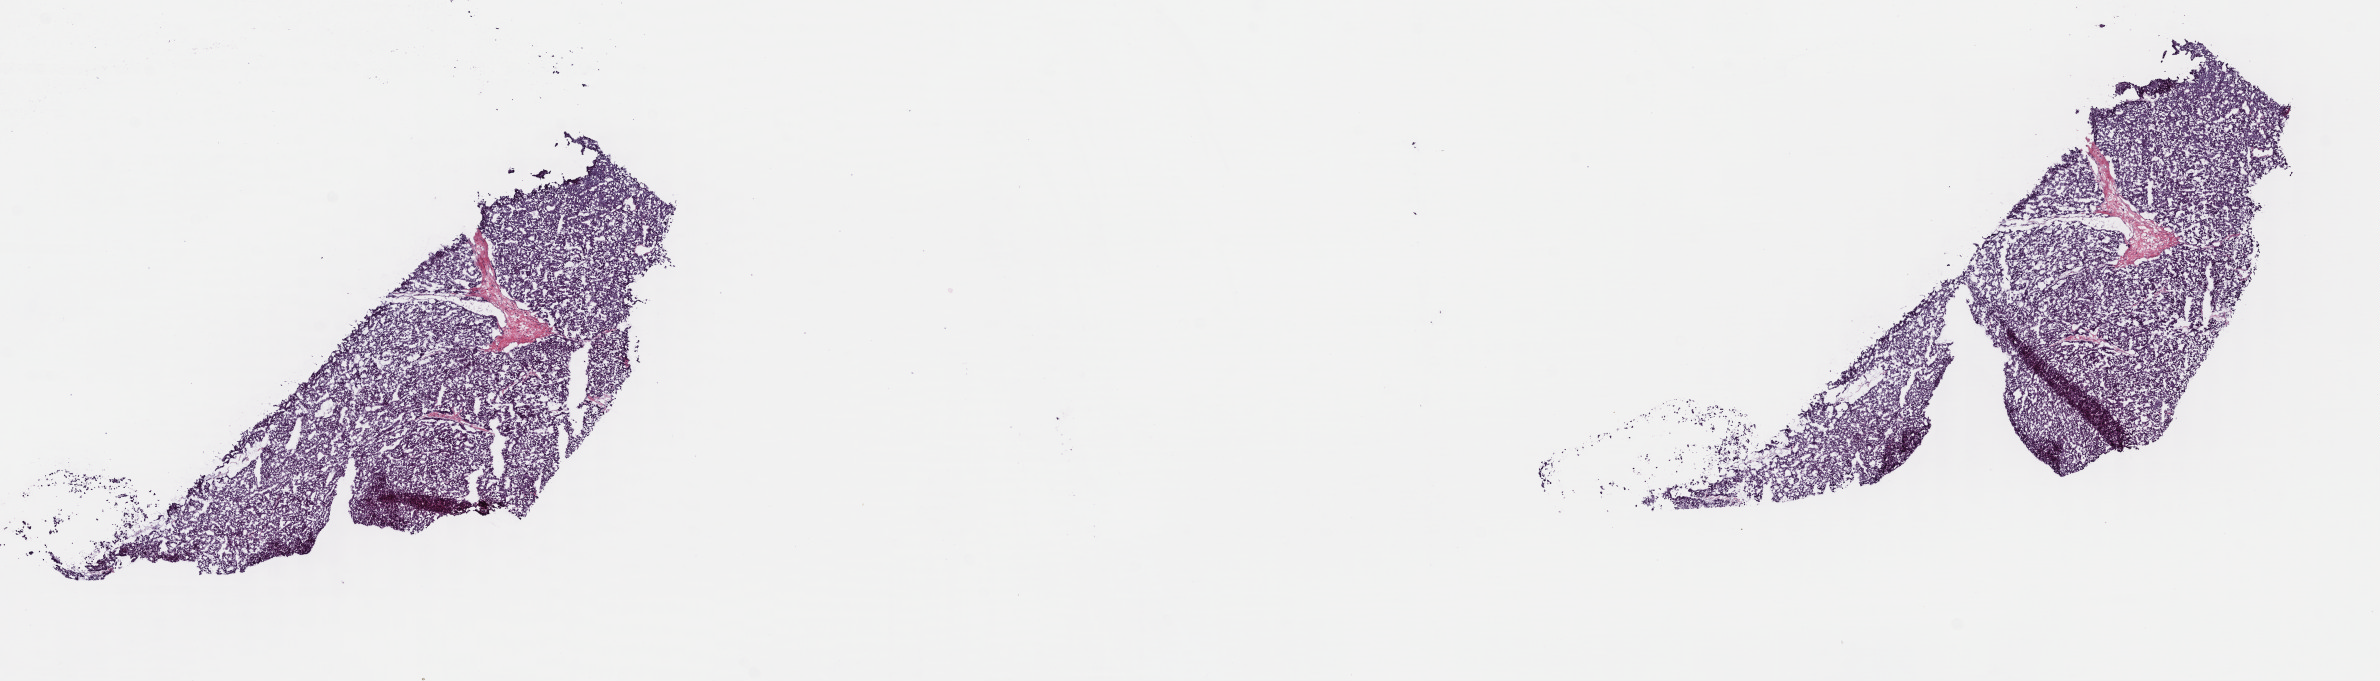
Whole-slide histology image, H&E, shown as a low-resolution overview of the whole scanned area (about 18.7 x 5.4 mm, slide scanned at 40x), frozen section from the top of the tissue portion, adrenal cortex, primary tumour sample. Female patient; age at initial diagnosis 36 years. Pathologist review of this section (percent, as recorded): tumour cells 90%, tumour nuclei 90%, normal cells 0%, stromal cells 5%, necrosis 5%. Infiltration values recorded for this section: lymphocyte infiltration 40%, monocyte infiltration 20%, neutrophil infiltration 20%.
• diagnosis: Adrenal cortical carcinoma (cortex of adrenal gland)